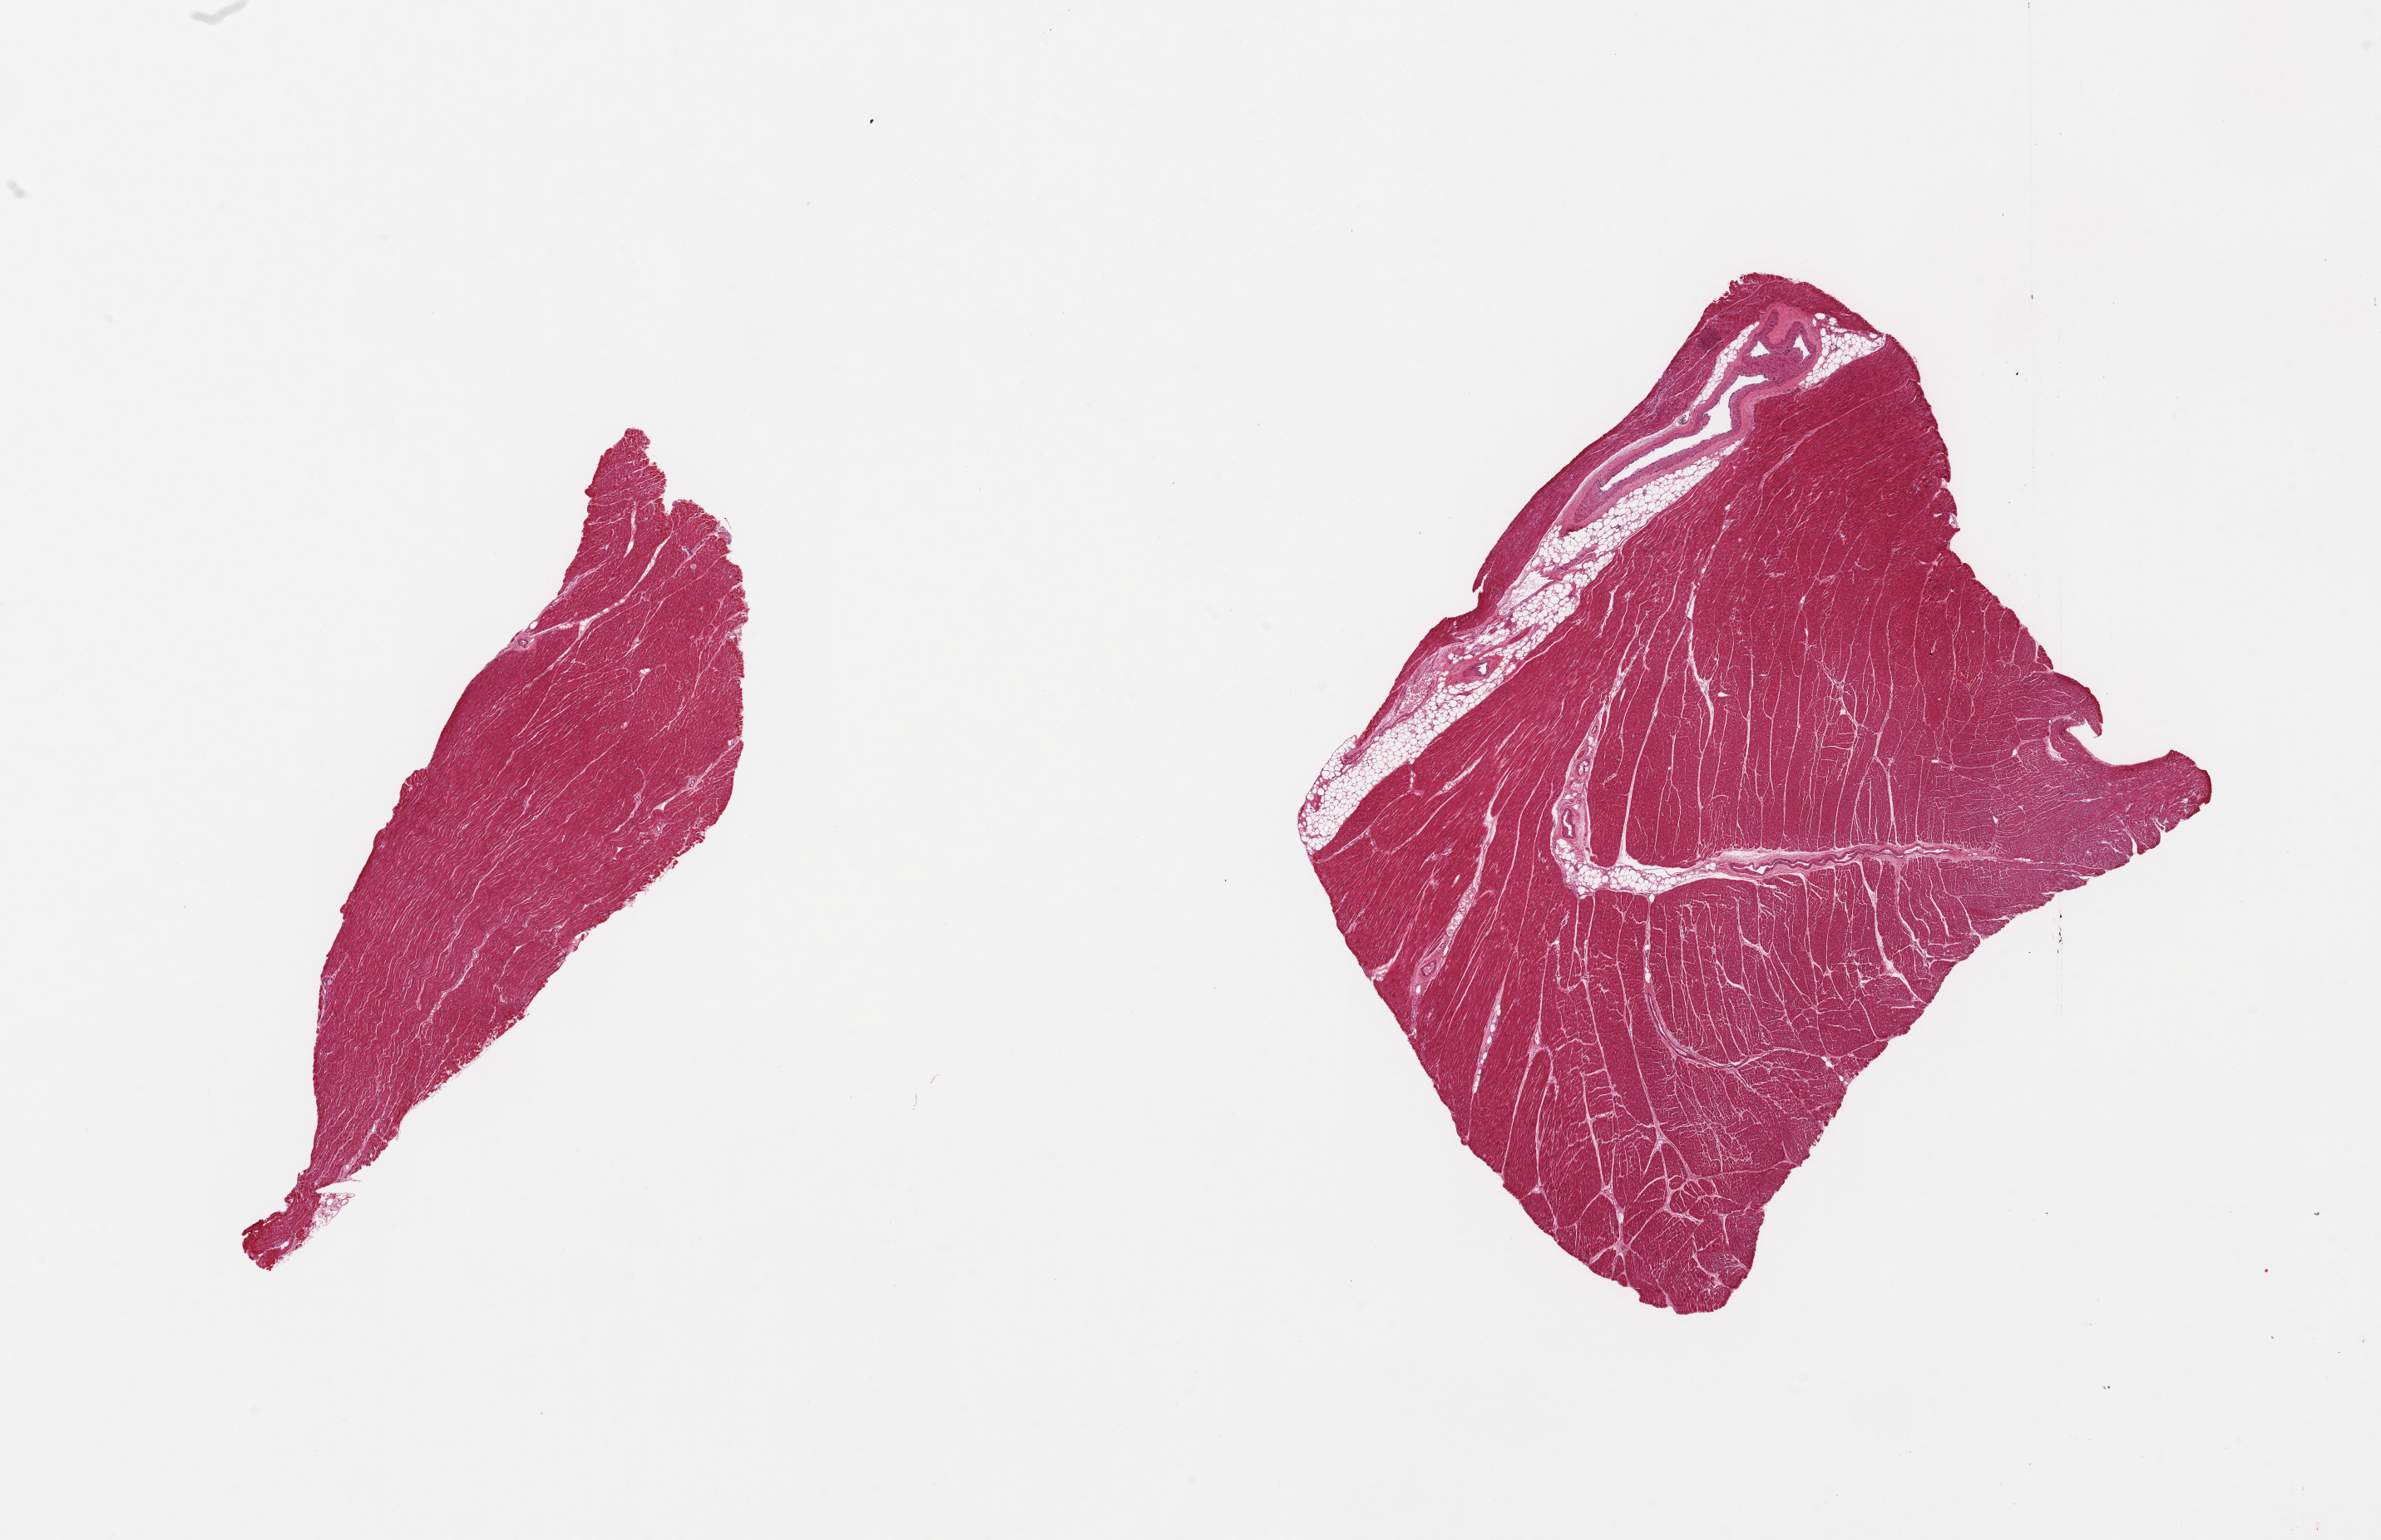
Whole-slide image, haematoxylin and eosin stain — whole scanned area (about 22.6 x 14.6 mm) shown as a low-resolution overview; PAXgene-fixed, paraffin-embedded tissue; section of heart (target tissue); tissue donor sample.
* reviewer comment on this tissue sample: 2 pieces; 1 piece includes 10% fat and vessels